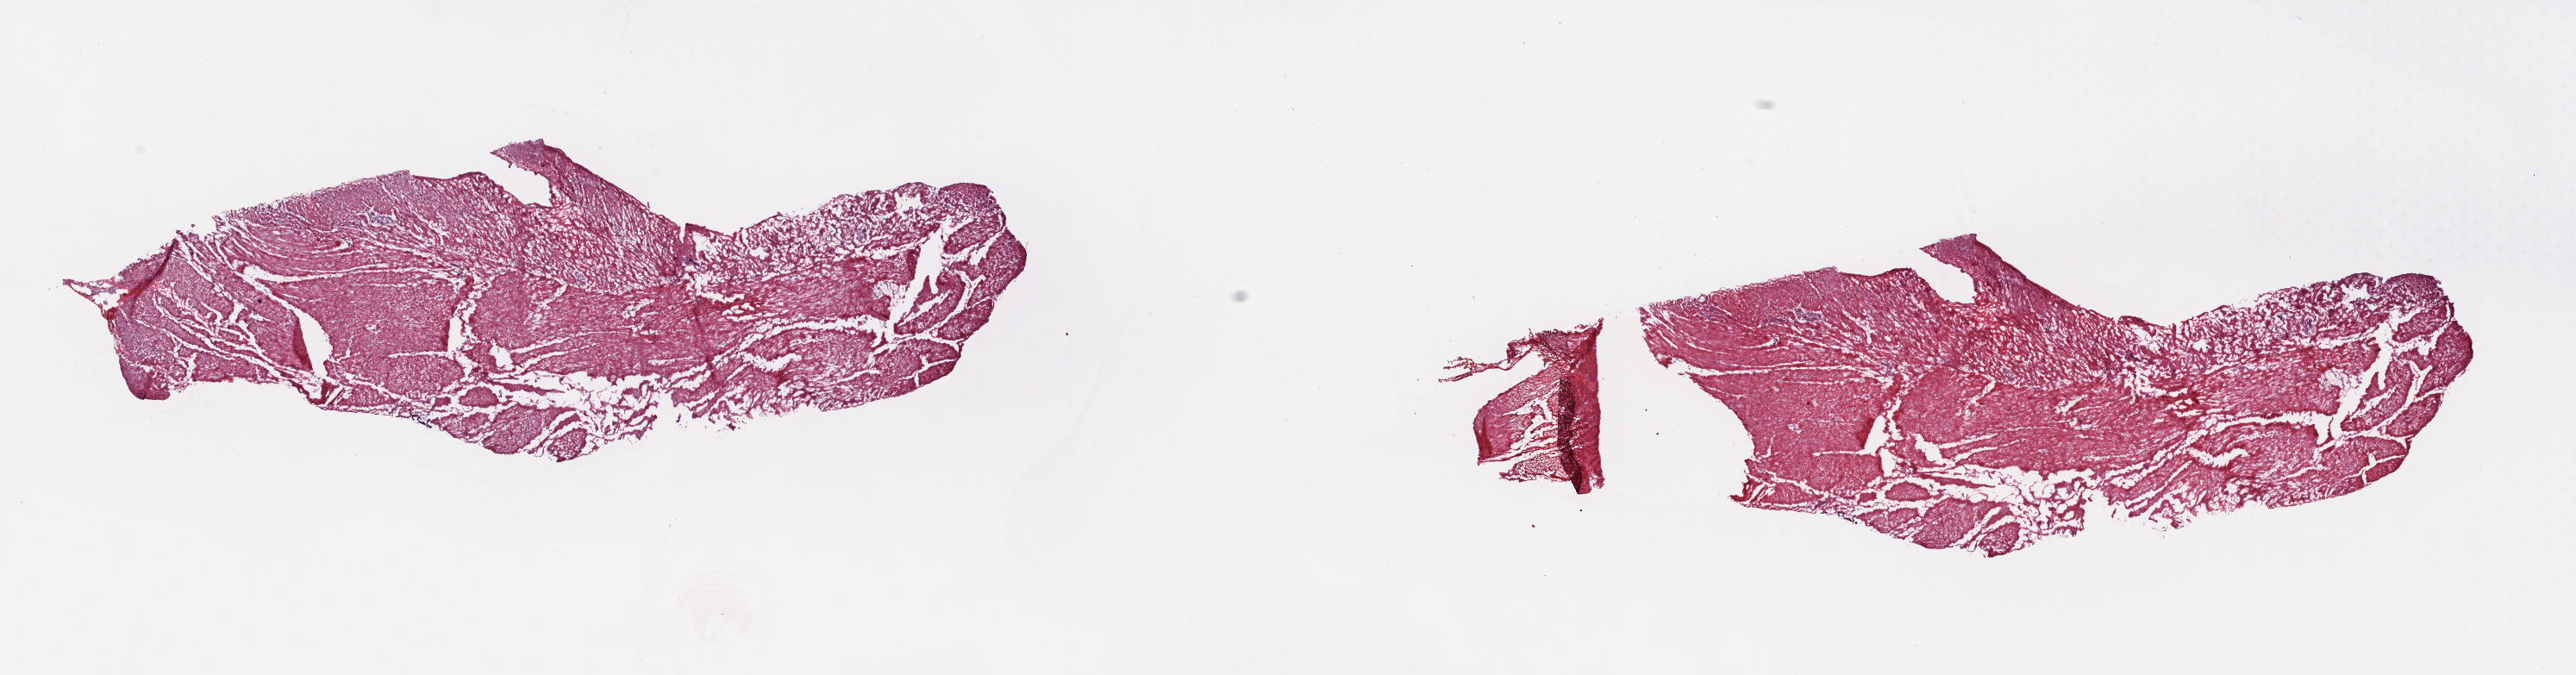
Whole-slide histology image, H&E-stained — a low-resolution overview of the entire scanned area, about 23.6 x 6.2 mm (acquisition: 20x scan). Frozen section from the top of the tissue portion. Solid tissue normal (non-tumour tissue) sample from the stomach. Male, age 68 years at initial diagnosis. Composition of this section per pathologist review: tumour cells 0%, tumour nuclei 0%, normal cells 100%, stromal cells 0%, necrosis 0%. Infiltration values recorded for this section: lymphocyte infiltration 1%, monocyte infiltration 0%, neutrophil infiltration 0%.
This section: solid tissue normal (non-tumour) sample from the same patient. Patient diagnosis: Carcinoma, diffuse type (gastric antrum).